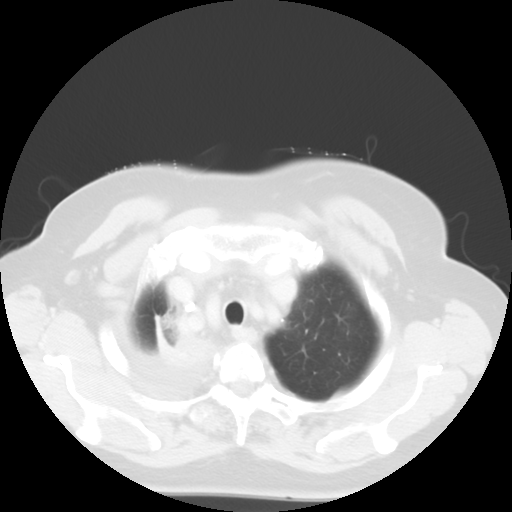
Chest CT, one axial slice. Position 46 of 52 along the scan axis. Reconstruction kernel STANDARD. 120 kVp. Lung window (W 1500 / L -600 HU). 512 × 512 image matrix, field of view 333 × 333 mm. Female patient, age 81 years. Case-level facts recorded for this patient, not image findings: clinical TNM (as recorded): T4 N3 M1b.
Outlined on this slice (rectangle marked by the reading radiologist):
- lung tumour (recorded histology: adenocarcinoma): bounding box <150,313,225,387> (left, top, right, bottom; pixels)